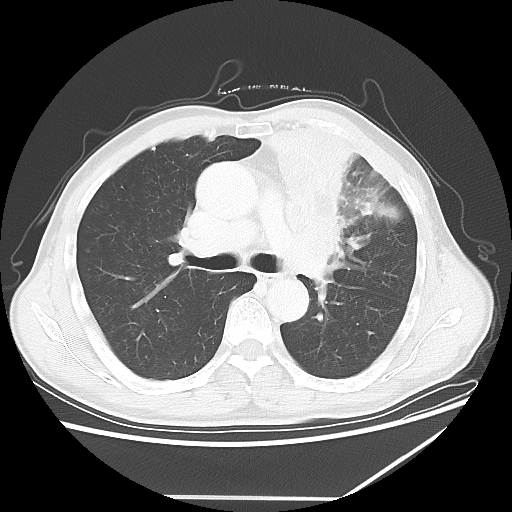
Chest CT, one axial slice; position 39 of 64 along the scan axis; reconstruction kernel LUNG; 100 kVp; lung window (W 1500 / L -600 HU); 5 mm slice thickness; 512 × 512 image matrix, field of view 383 × 383 mm. Male patient, age 64 years. Case-level facts recorded for this patient, not image findings: clinical TNM (as recorded): T1c N1 M1; histopathological grade: G2.
Structures marked on this image (bounding box drawn by a radiologist):
- lung tumour (recorded histology: squamous cell carcinoma): bounding box (x1, y1, x2, y2) in pixels: (236, 96, 375, 286)